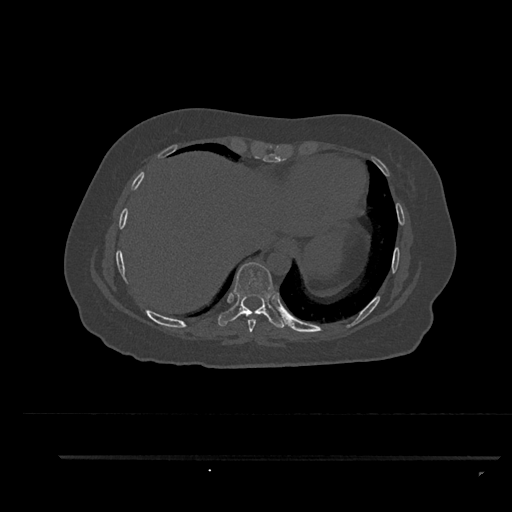
CT including the spine, one axial slice. Position 426 of 797 along the scan axis. Reconstruction kernel Br40s/3. Bone window (W 1800 / L 400 HU). 0.5 mm slice thickness. 512 × 512 image matrix. Patient: female, 44 years. Case-level facts recorded for this patient, not image findings: primary cancer: renal.
Structures marked on this image (semi-automatic segmentation, software-assisted and operator-edited):
- T8 vertebra: bounding box [x1, y1, x2, y2] px = [247, 311, 258, 333]
- T9 vertebra: [218, 262, 286, 328]